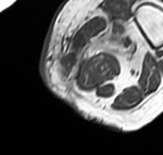
MRI of an extremity soft-tissue mass, one axial slice; position 11 of 65 along the scan axis; MR volume resampled by the dataset authors to the PET/CT grid (not the native acquisition matrix); 3.27 mm slice thickness; 163 × 155 image matrix. Female patient. From the clinical record (not read from this slice): histological type: pleomorphic leiomyosarcoma; grade: high; site of the primary tumour: left thigh.
Structures marked on this image (expert contour drawn on MRI and transferred to this co-registered scan by the dataset authors):
- gross tumour volume including surrounding oedema: bounding box [x1, y1, x2, y2] px = [60, 10, 143, 82]